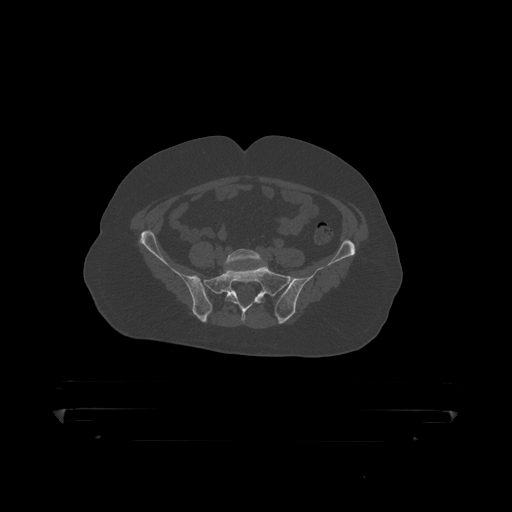
CT including the spine, one axial slice; reconstruction kernel STANDARD; 120 kVp; bone window (W 1800 / L 400 HU); 512 × 512 image matrix, field of view 650 × 650 mm. Patient: male, 60 years. Case-level facts recorded for this patient, not image findings: primary cancer: prostate.
Annotated regions visible in this slice (semi-automatic segmentation, software-assisted and operator-edited):
- L5 vertebra: bounding box <224,249,265,268> (left, top, right, bottom; pixels)